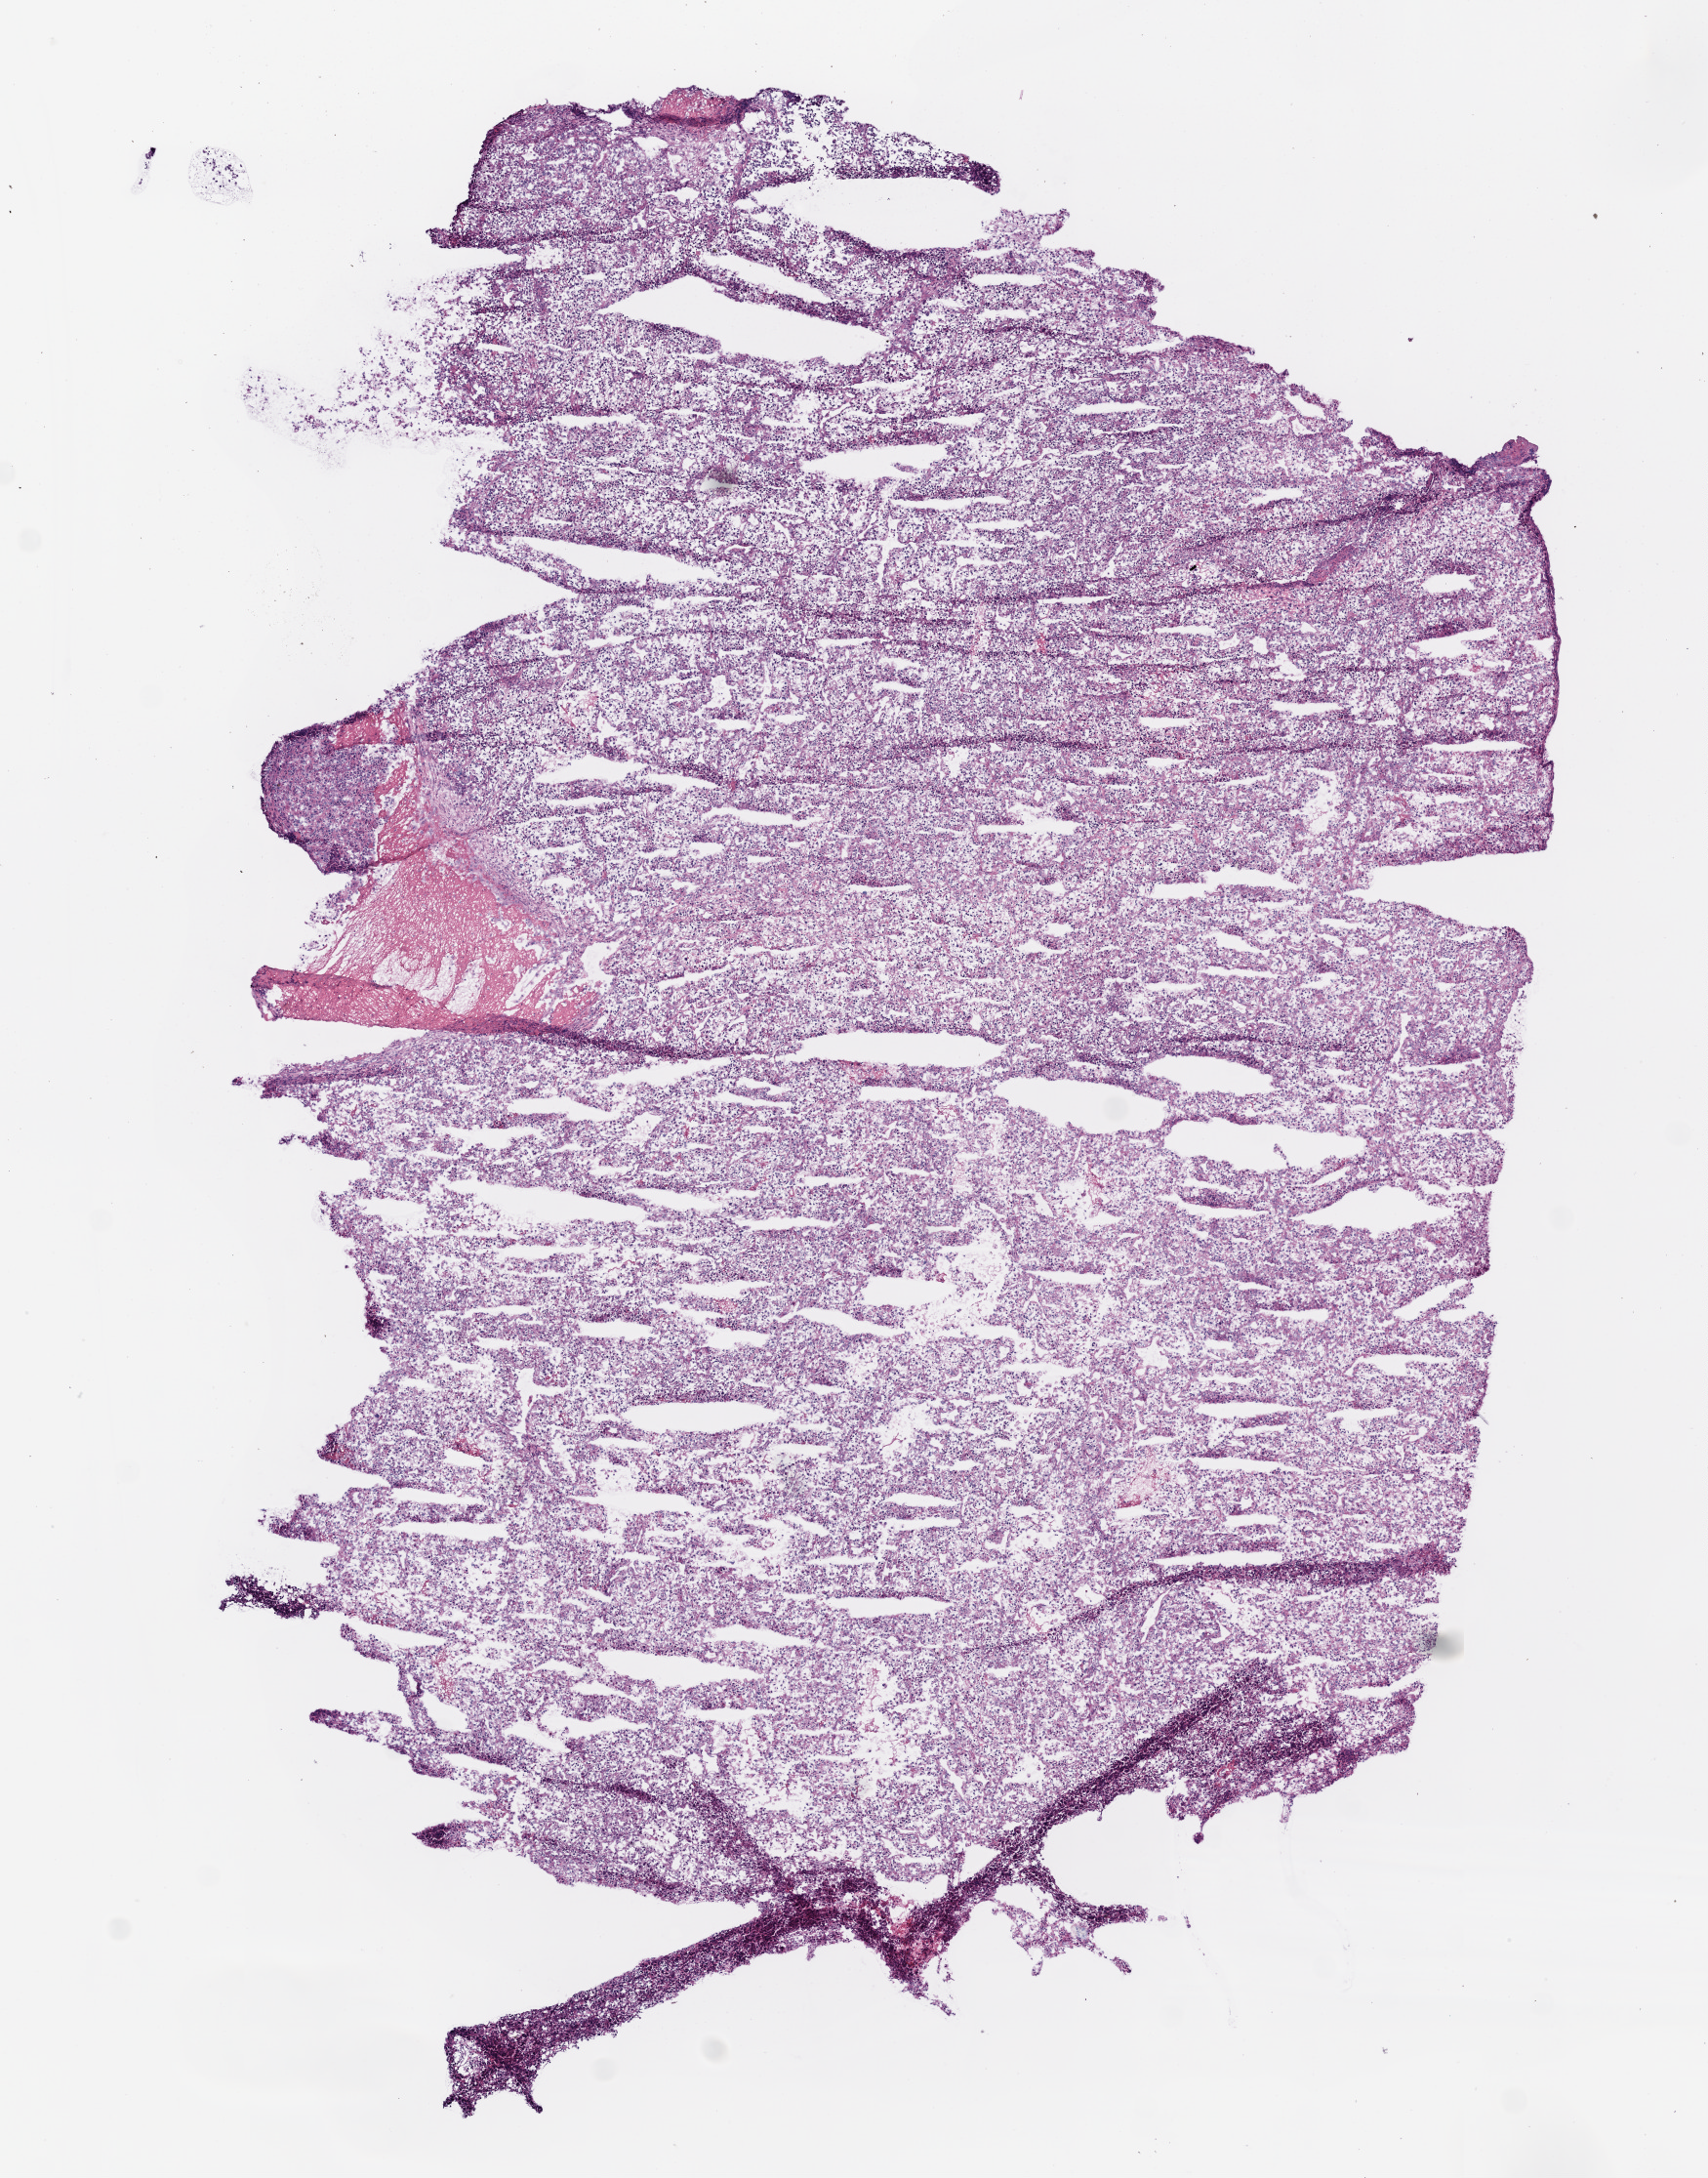
Digitized H&E-stained tissue section (whole slide), a low-resolution overview of the entire scanned area, about 7.0 x 9.0 mm; frozen section from the top of the tissue portion; sample: primary tumour, kidney. Patient: female, age at initial diagnosis 66 years. Histologic grade: G3 (poorly differentiated). Pathologist review of this section (percent, as recorded): tumour cells 90%, tumour nuclei 85%, normal cells 0%, stromal cells 10%, necrosis 0%.
• AJCC pathologic stage: IV
• laterality: left
• diagnosis: Clear cell adenocarcinoma, NOS